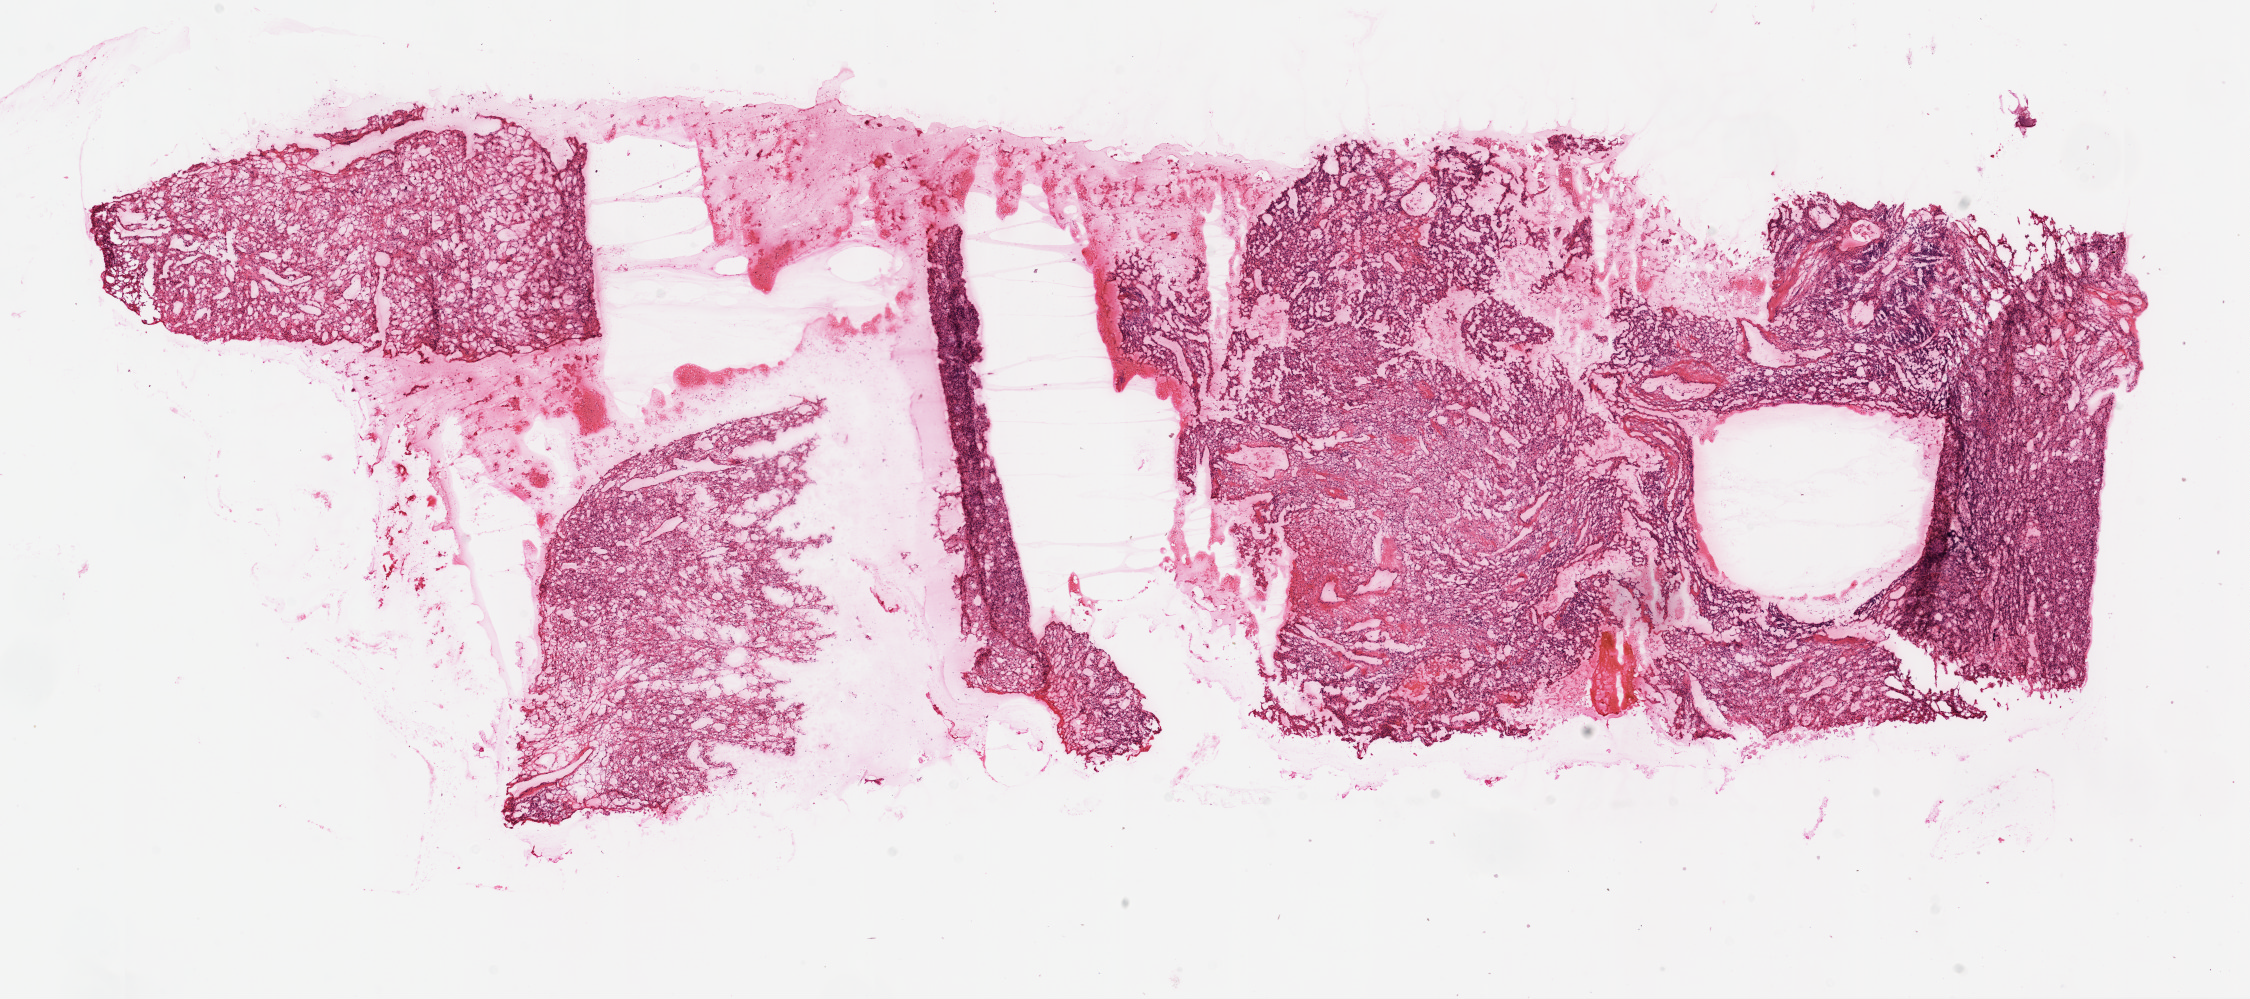
Digitized H&E tissue section (whole slide) — whole scanned area (about 18.1 x 8.0 mm, slide scanned at 20x) shown as a low-resolution overview; frozen section from the top of the tissue portion; primary tumour sample from the kidney. Patient: female, age at initial diagnosis 42 years. Histologic grade: G3 (poorly differentiated). Pathologist review of this section (percent, as recorded): tumour cells 90%, tumour nuclei 85%, normal cells 0%, stromal cells 10%, necrosis 0%.
TNM: T1a NX M0. AJCC pathologic stage: I. Histologic diagnosis: Clear cell adenocarcinoma, NOS.